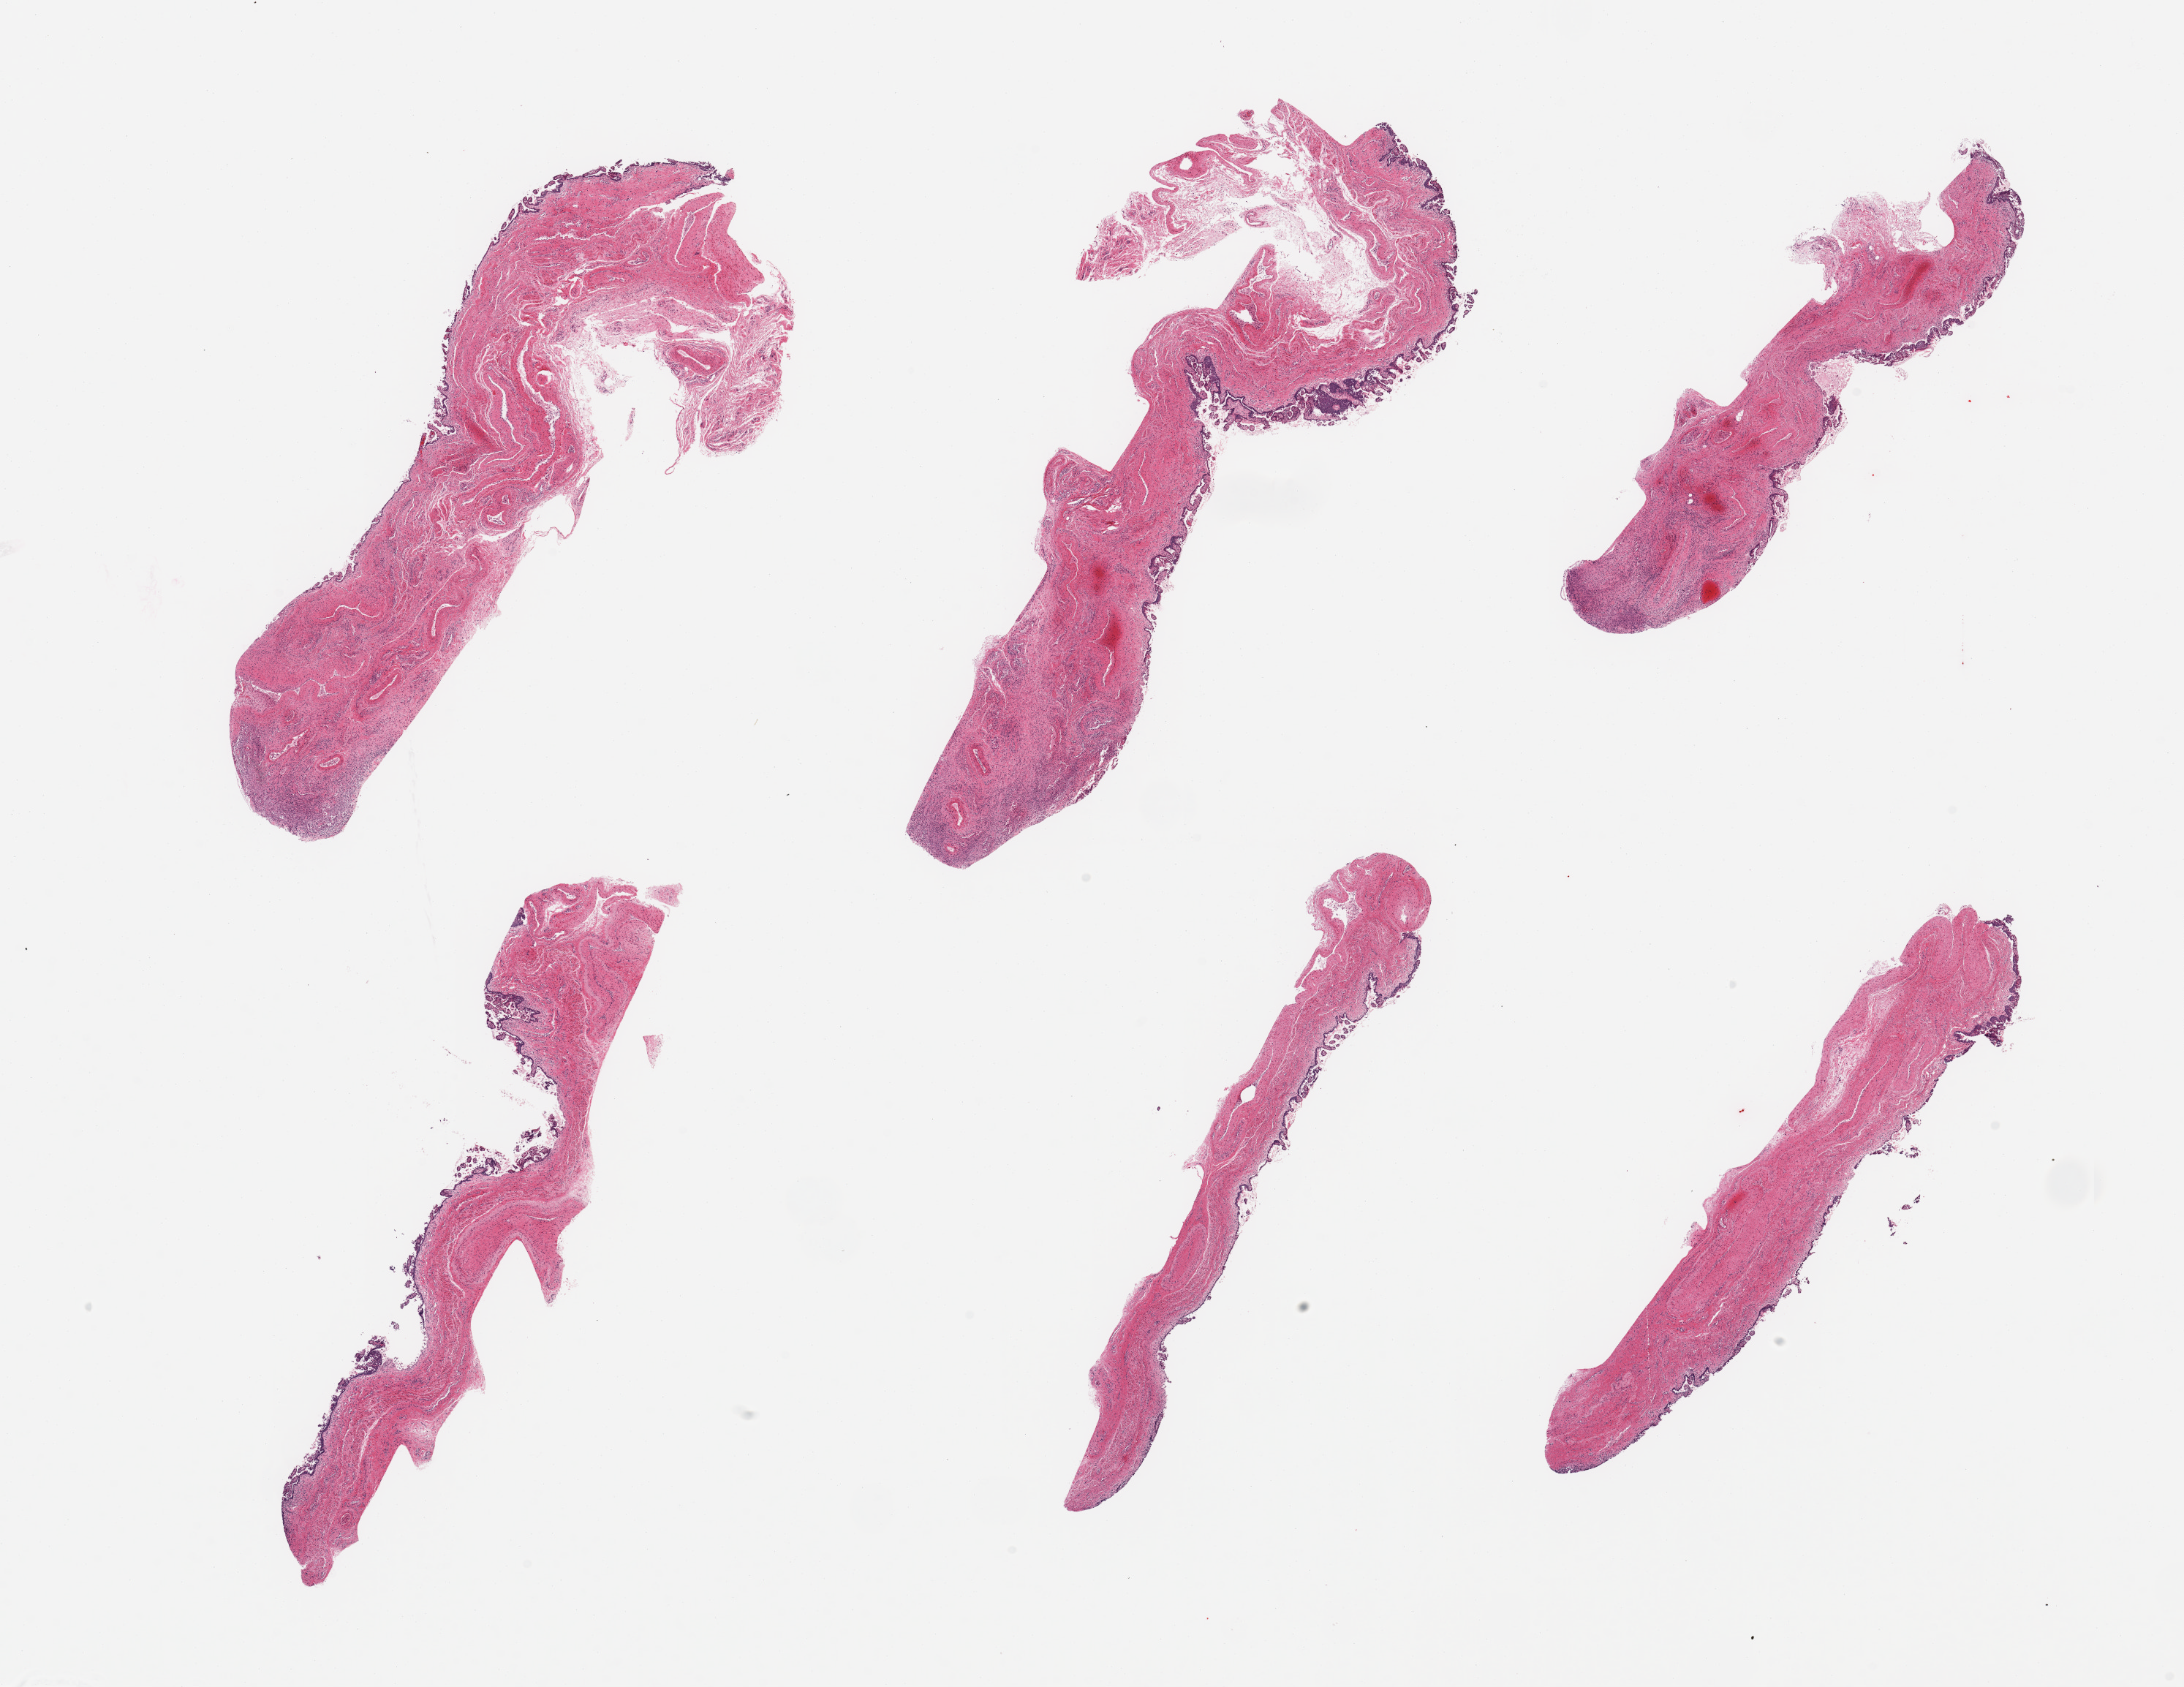
Whole-slide image, hematoxylin and eosin (H&E) stain, brightfield — a low-resolution overview of the entire scanned area, about 23.6 x 18.2 mm. PAXgene-fixed, paraffin-embedded tissue. Section of esophageal mucous membrane (target tissue). Tissue donor sample. Male donor.
Review note (as recorded): 6 pieces; moderate to severe autolysis; largely sloughed mucosa; thick-walled vessels in submucosa; congestion.